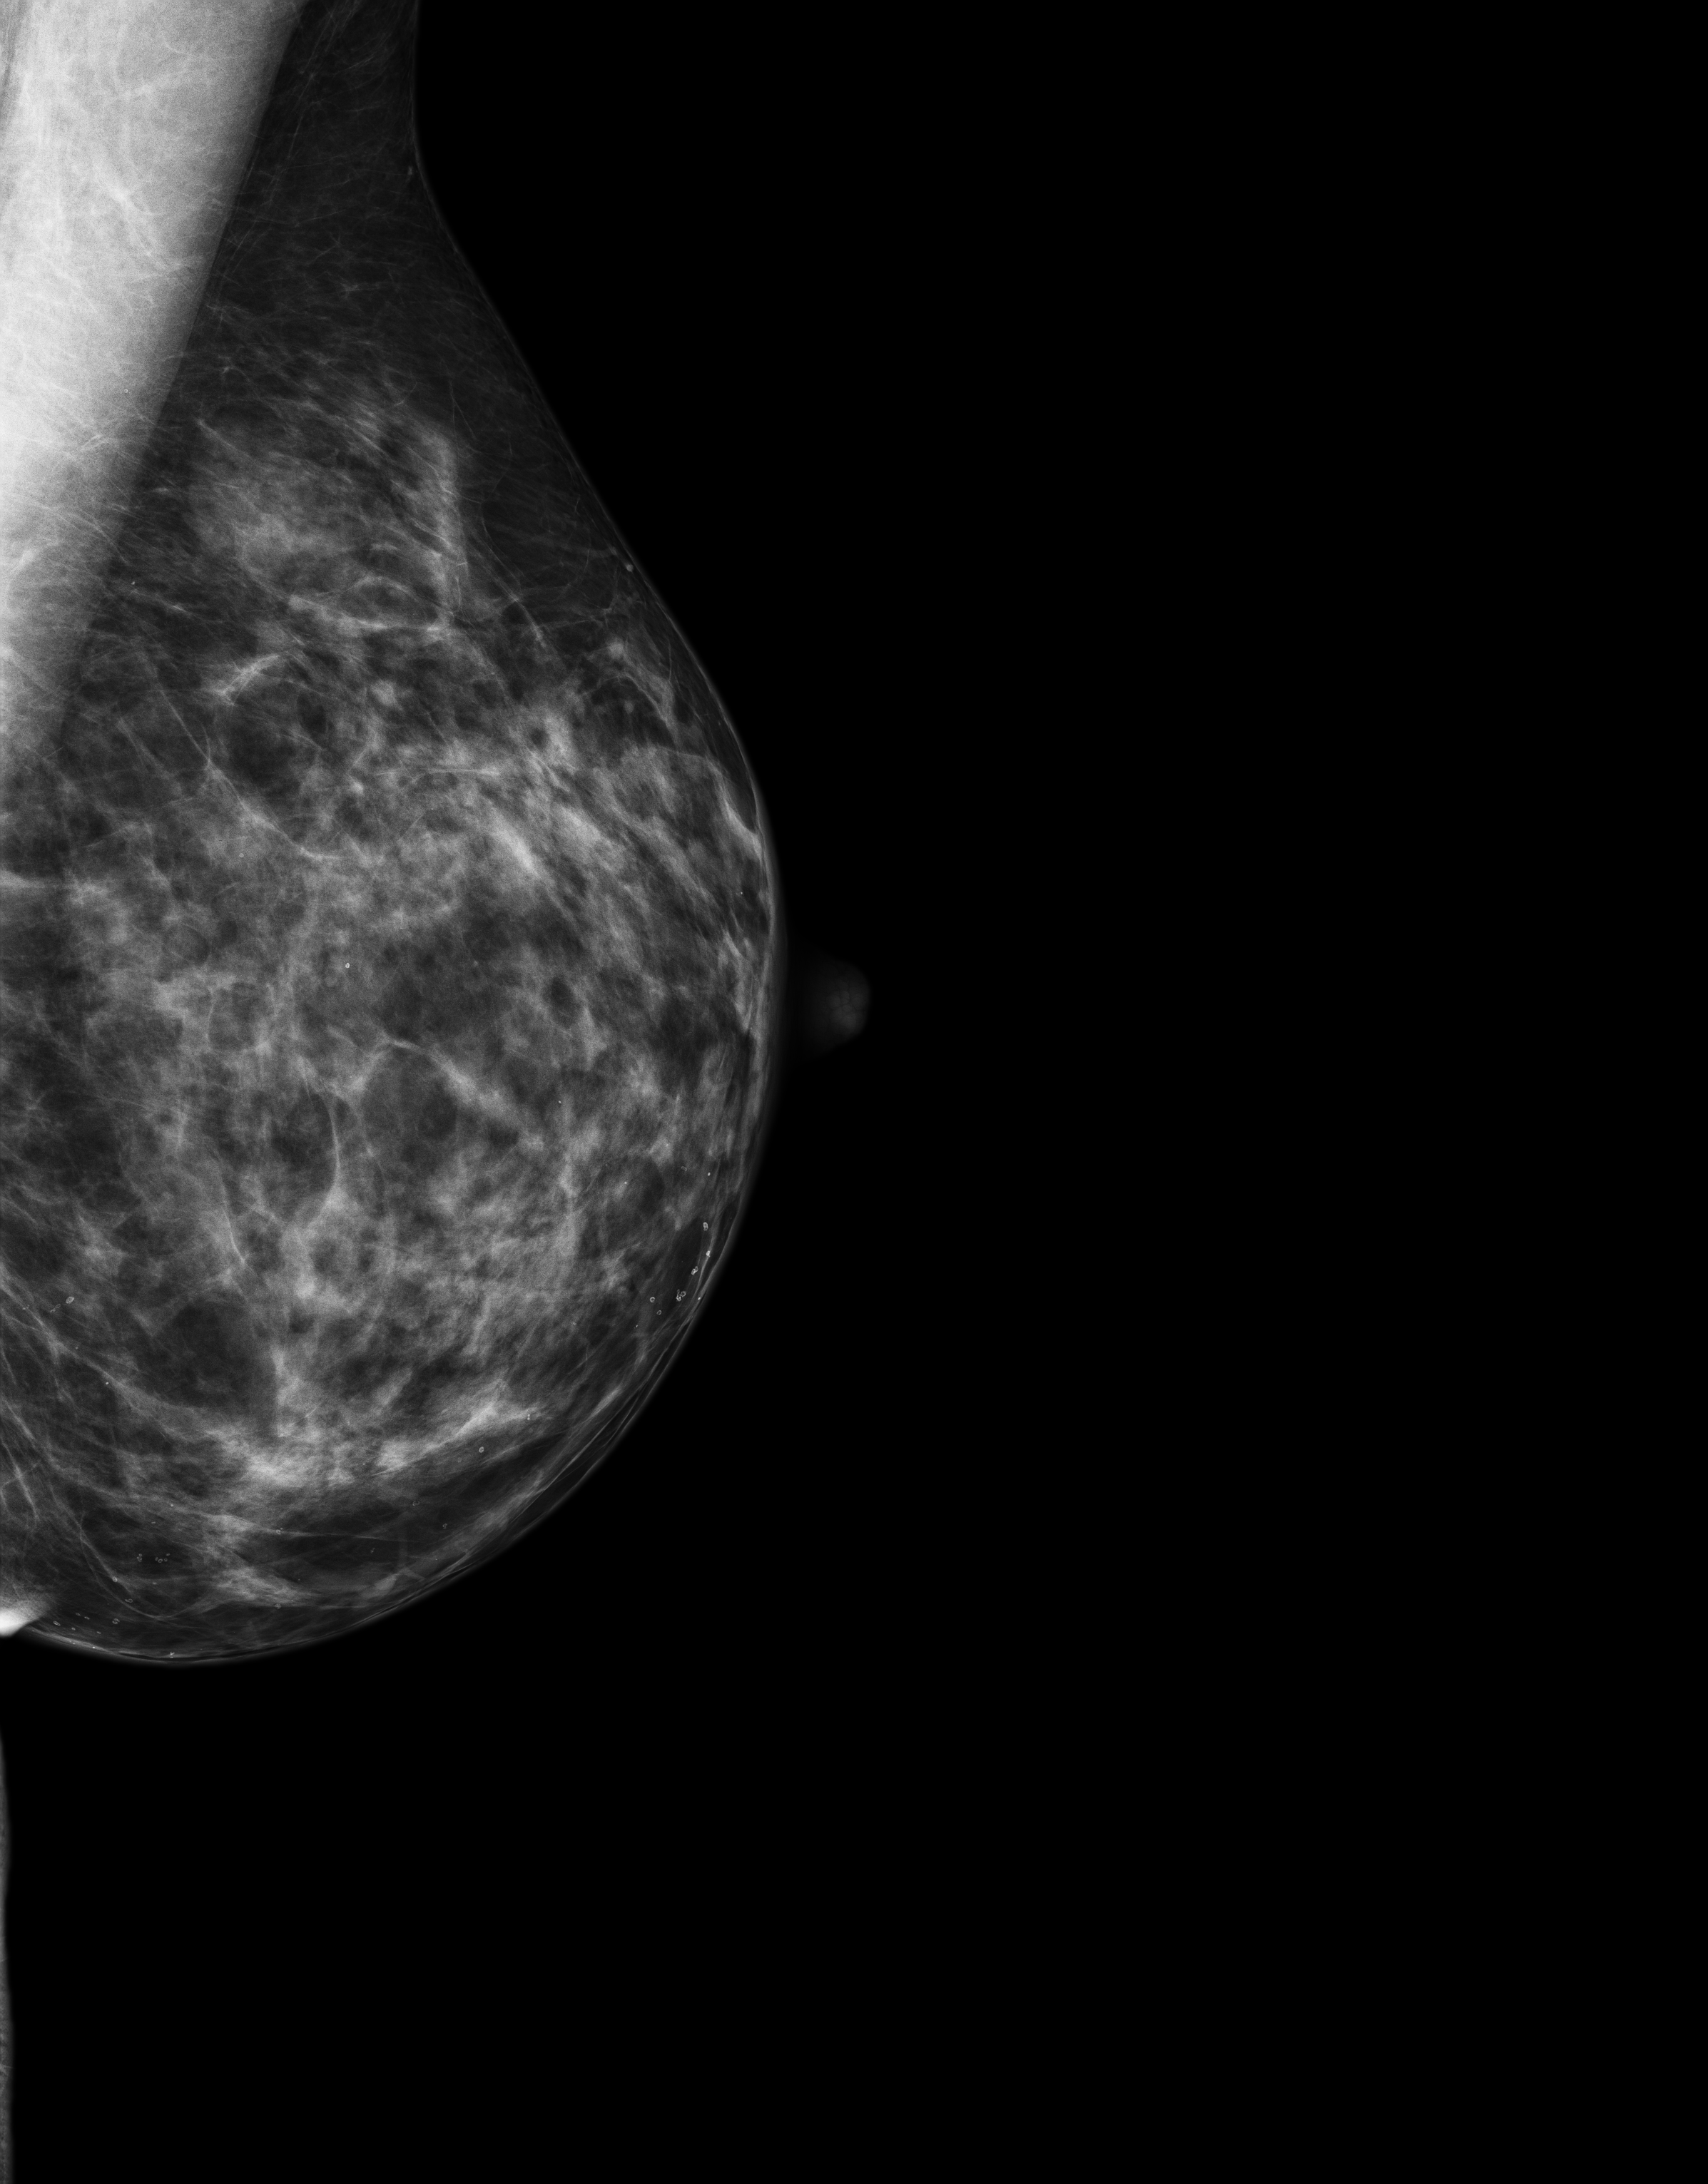
Full-field digital mammogram (FFDM), left breast, MLO view, annual screening mammography examination, compressed breast thickness 59 mm, system: Senographe Essential ADS_56.21.3. Patient aged 46 years (female).
Breast density at the screening exam (both breasts): heterogeneously dense (BI-RADS density category c). Final BI-RADS assessment for this screening round (tomosynthesis exam, both breasts): category 2. Recall: no recall after this screen.